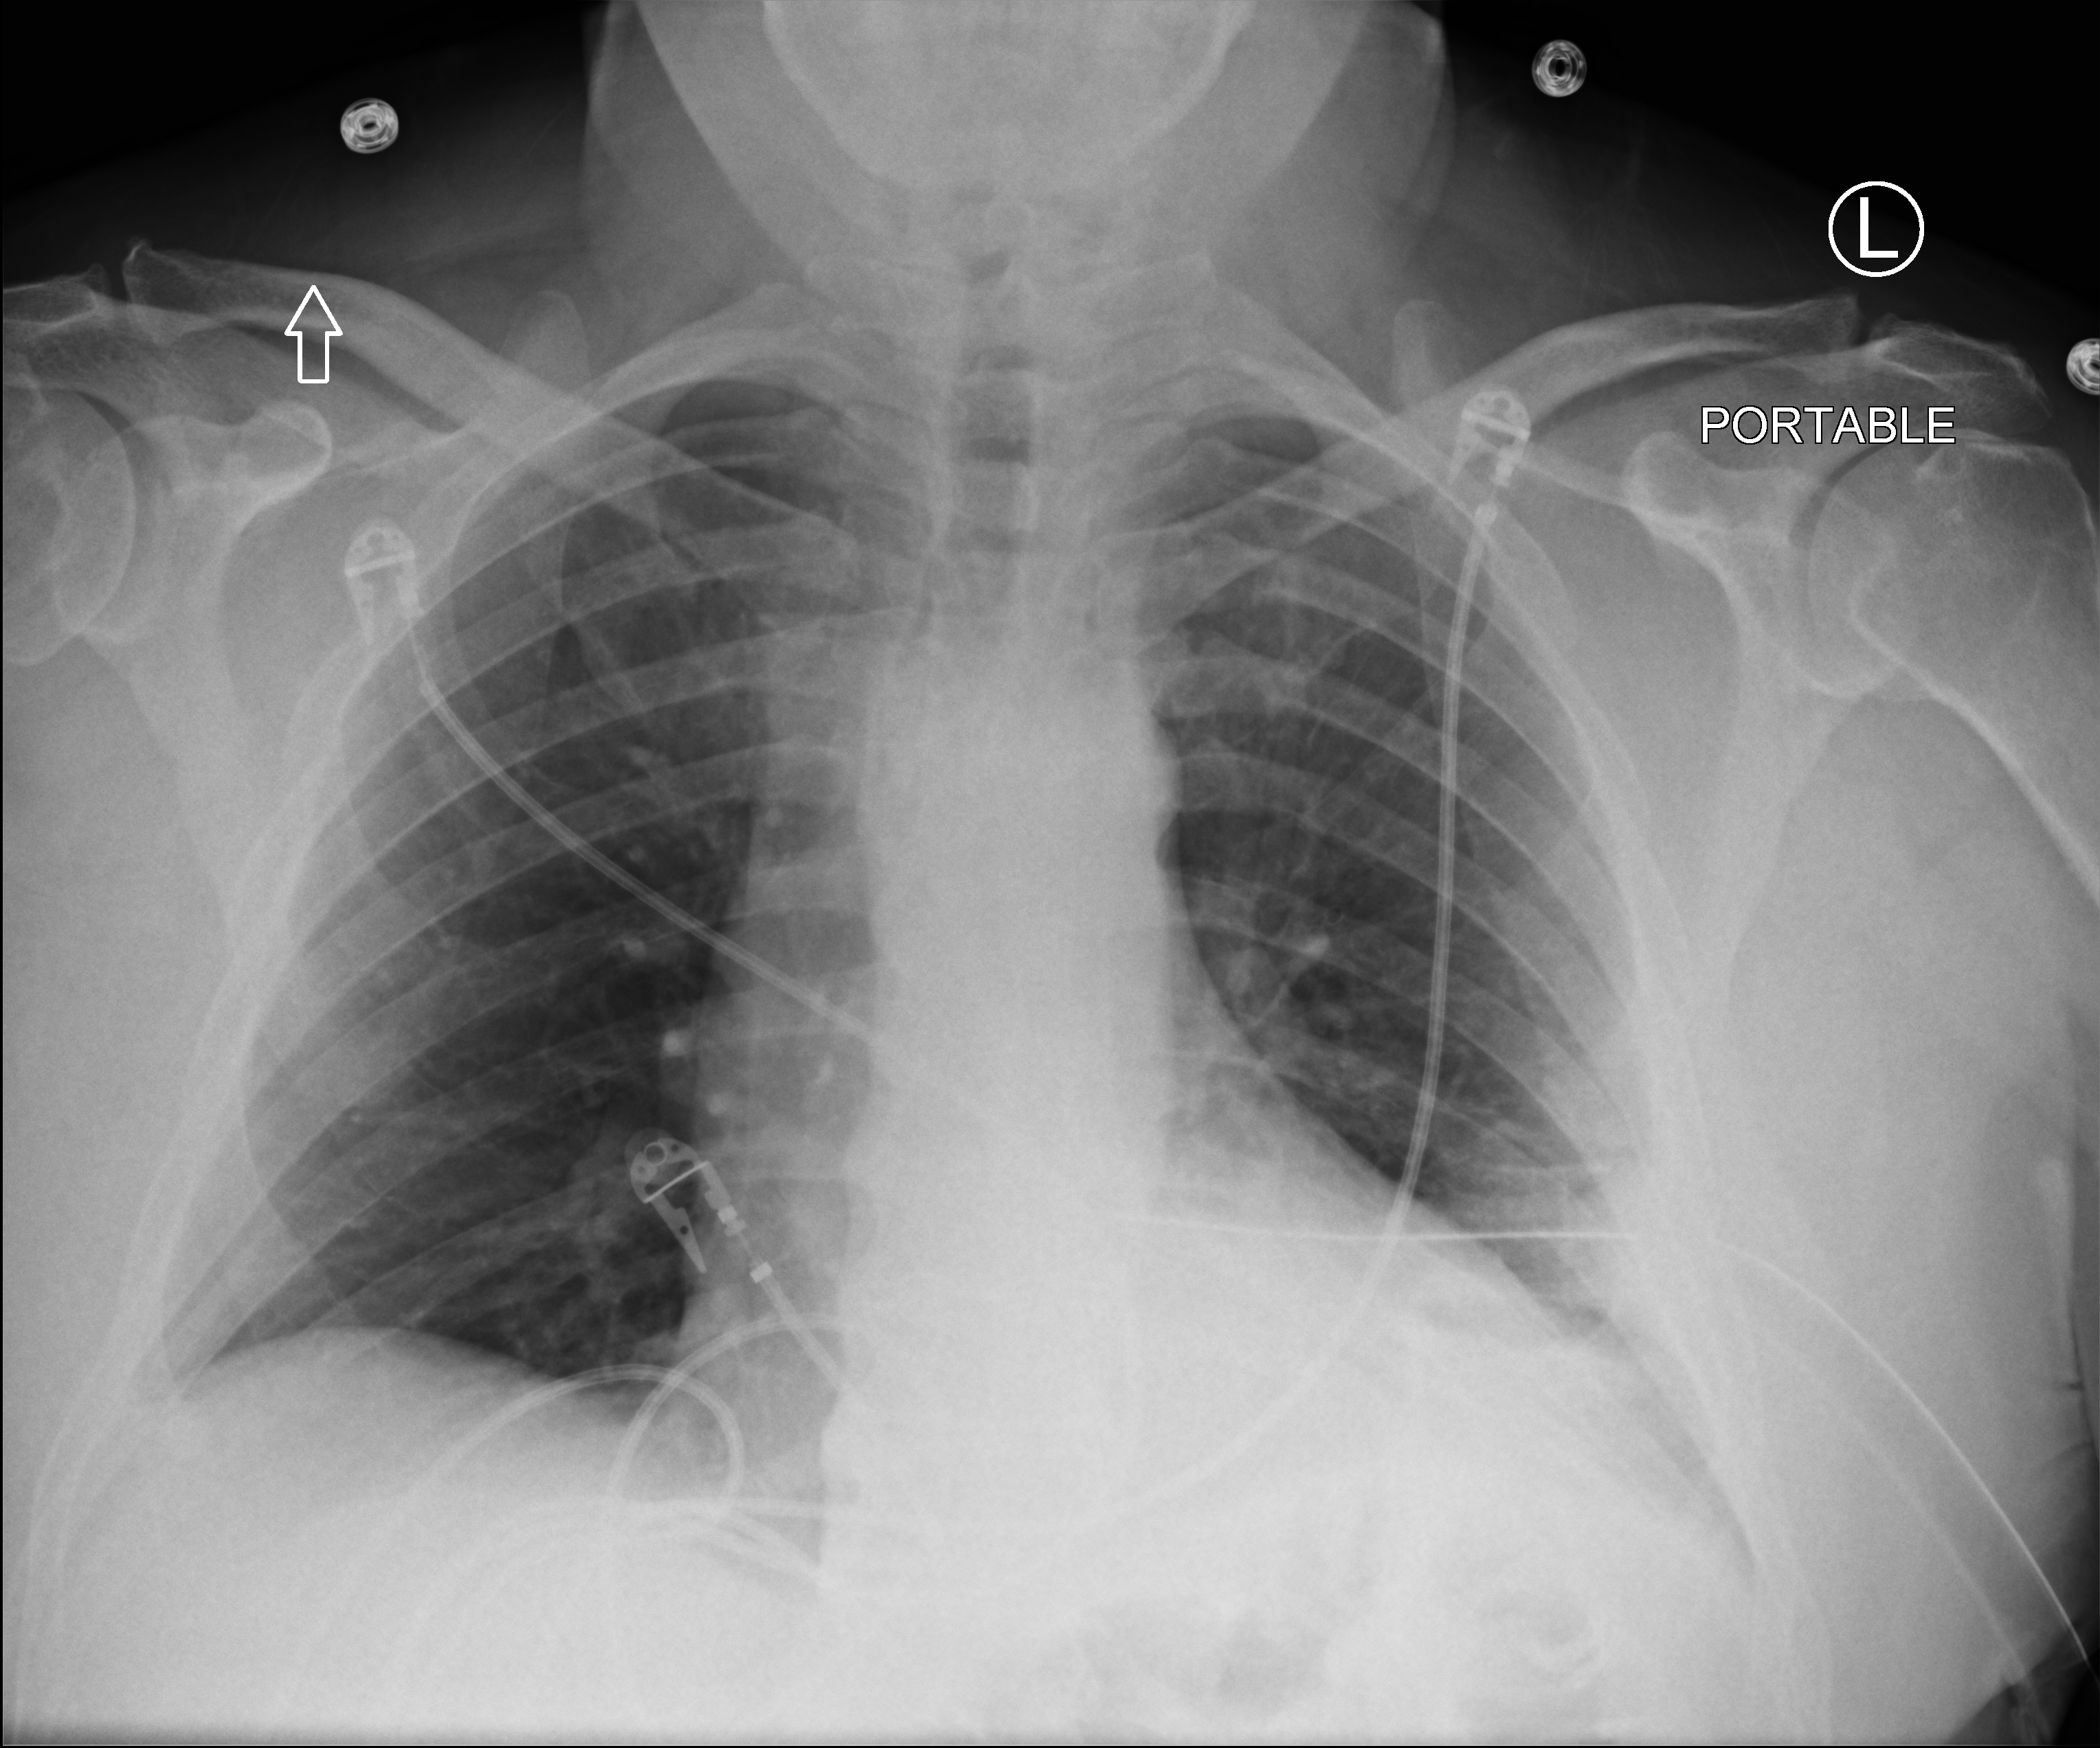
Chest X-ray (portable). Patient hospitalised with COVID-19; male, aged 18–59 years.
From the hospital-stay record, not from the radiograph (when in the stay this image was taken is not recorded):
- mechanically ventilated during this hospital stay: no
- admitted to intensive care during this hospital stay: no